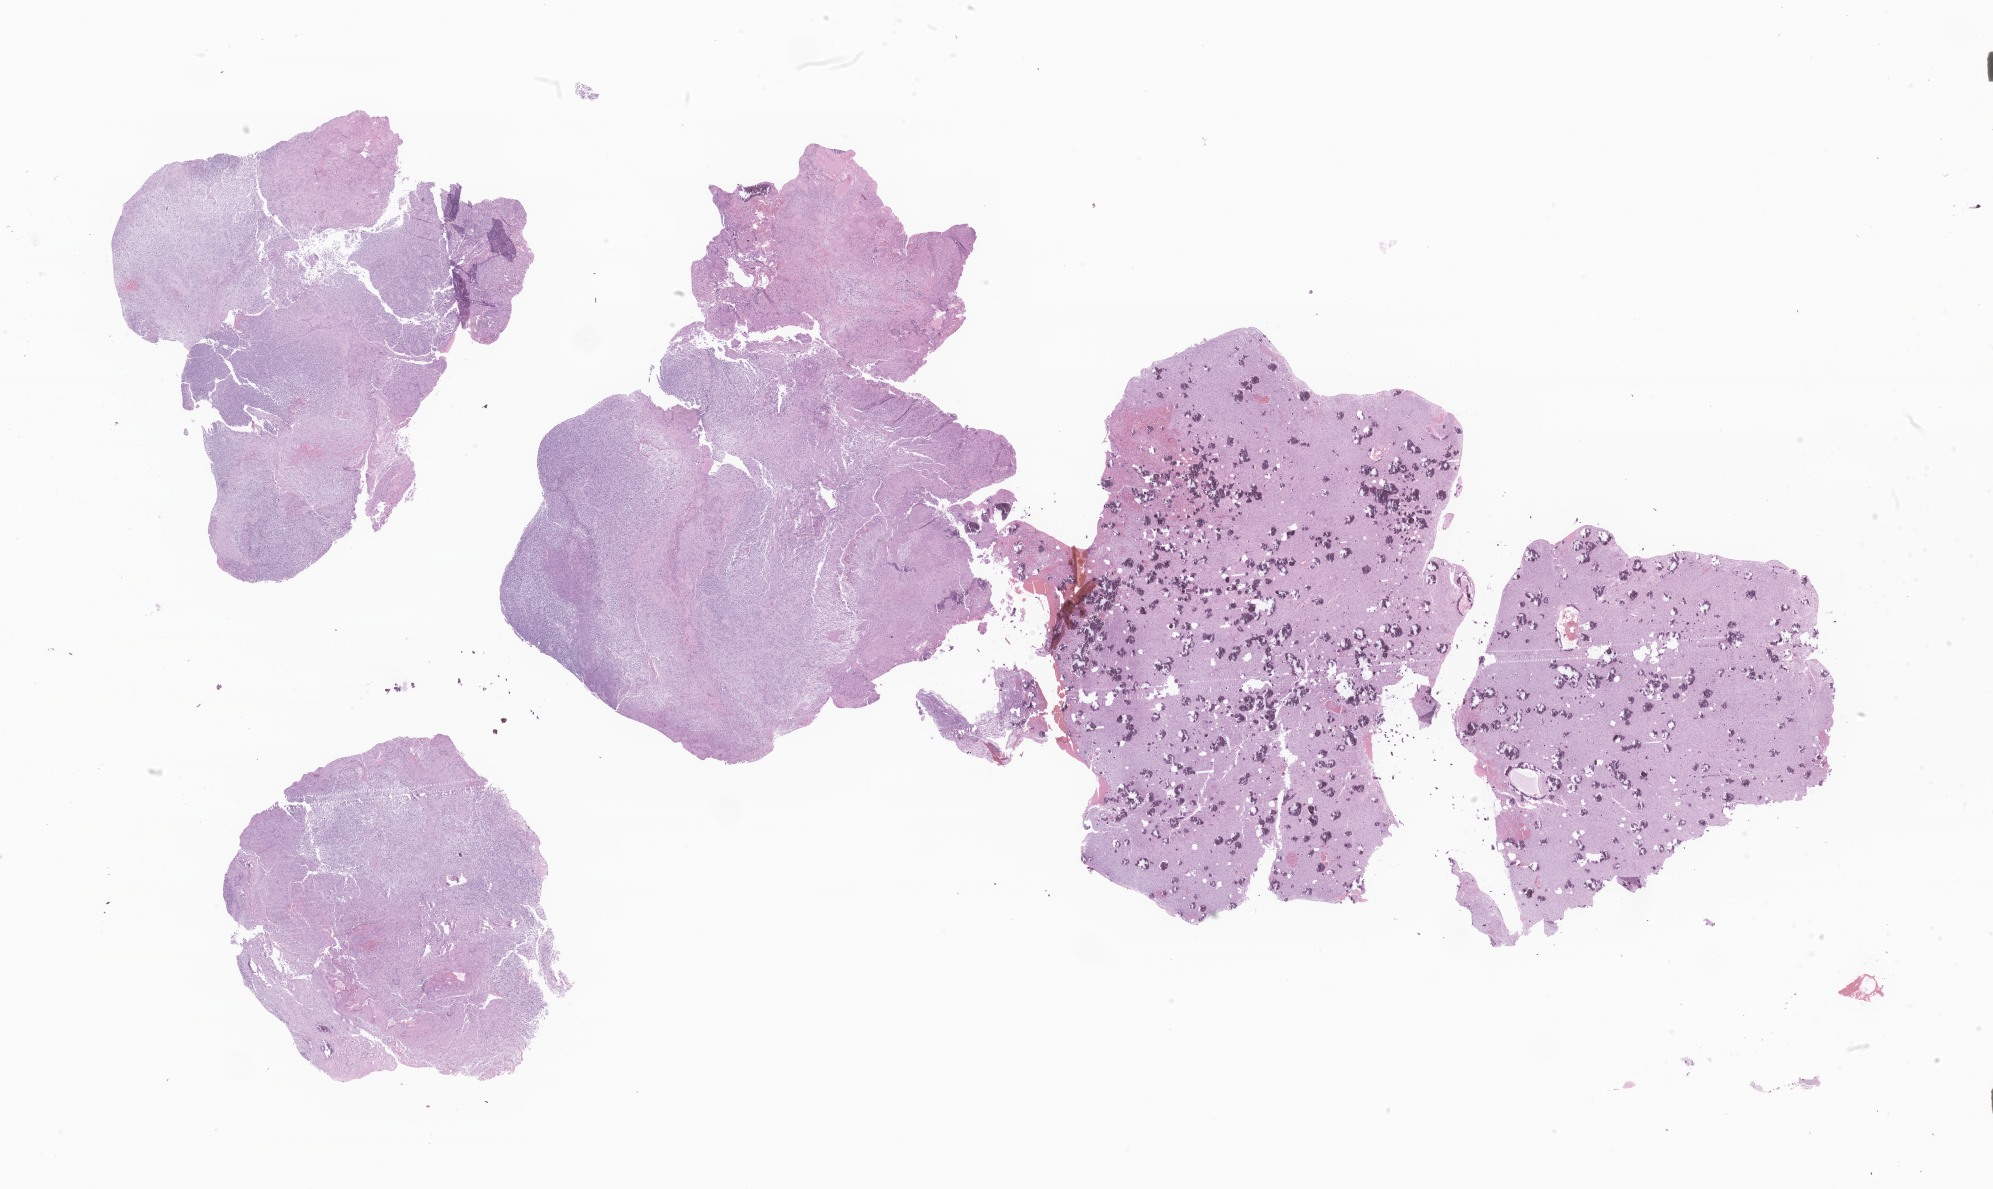
Digitized haematoxylin and eosin-stained section of tumor tissue from the brain, whole scanned area (about 33.6 x 20.1 mm) shown as a low-resolution overview, formalin-fixed, paraffin-embedded (FFPE) tissue. Patient female; age 75 months (6 years 3 months).
Diagnosis (ICD-O-3 morphology term): Glioma, malignant.